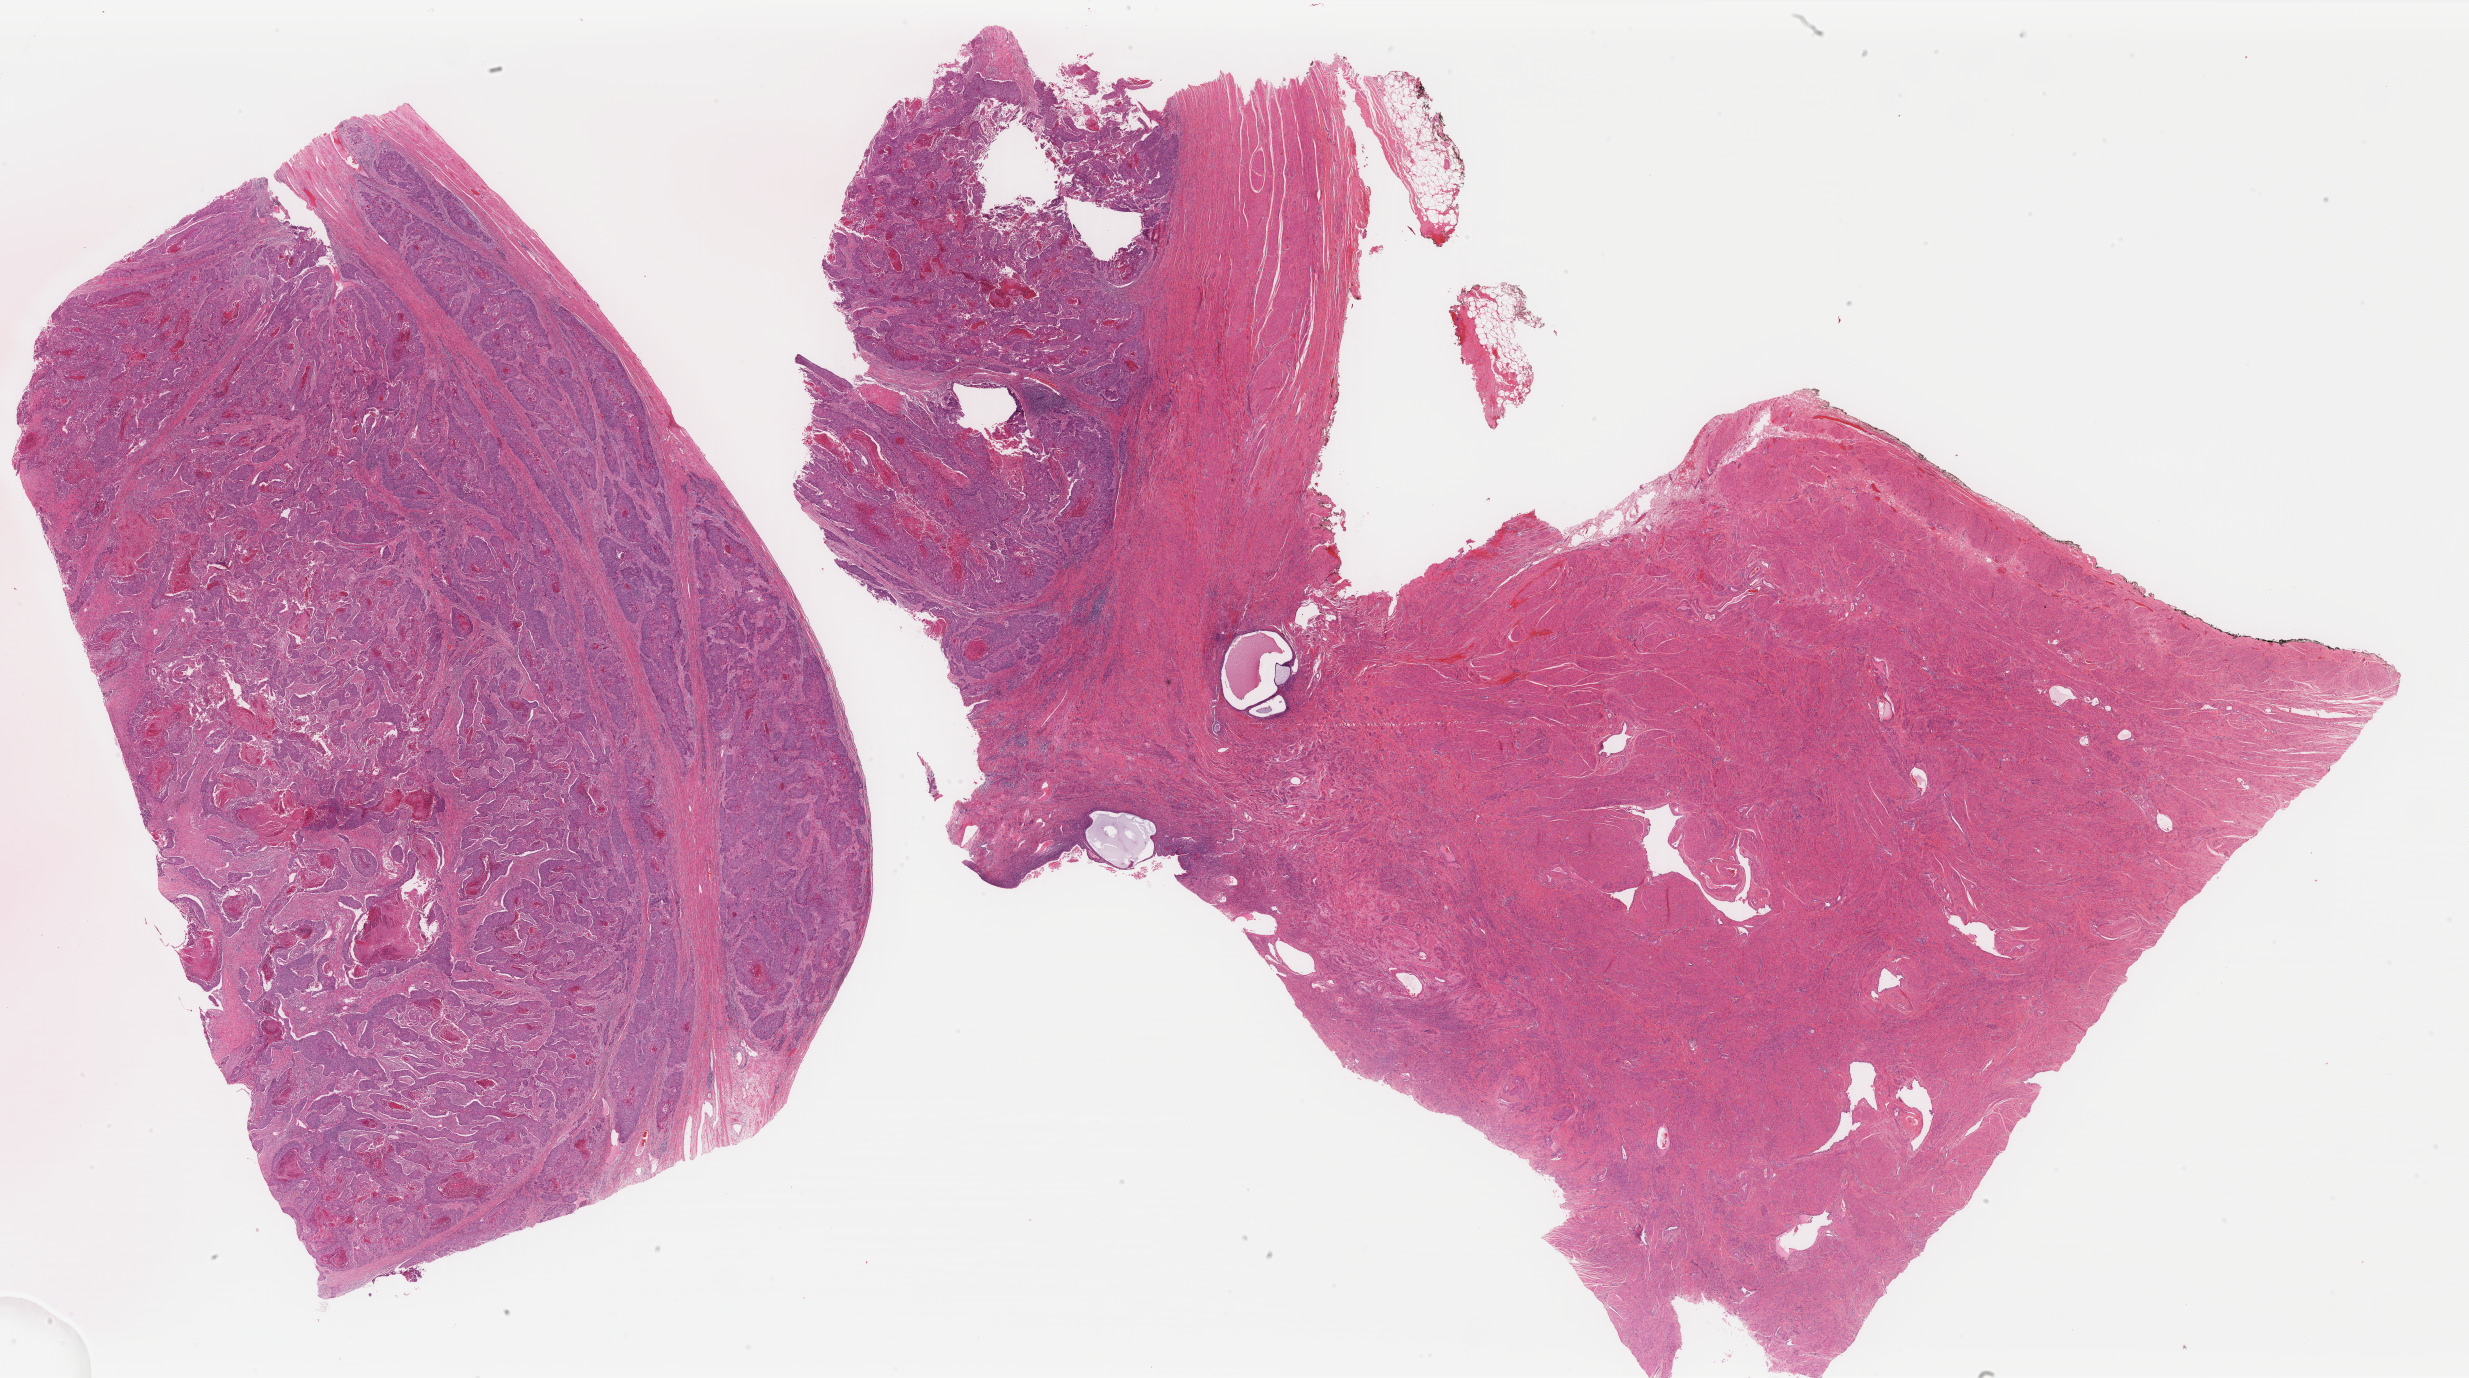
Whole-slide histology image, Hematoxylin and eosin (H&E) stained, a low-resolution overview of the entire scanned area, about 39.2 x 21.9 mm, FFPE section, primary tumour sample from the cervix. Female patient; age at initial diagnosis 46 years. Histologic grade: G3 (poorly differentiated).
FIGO stage: IIIB. Diagnosis: Squamous cell carcinoma, NOS (cervix uteri).